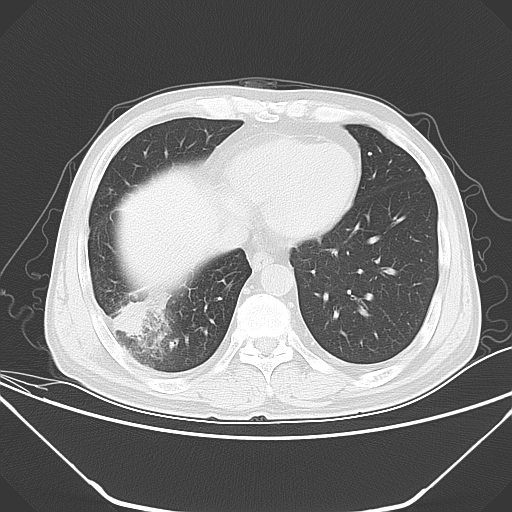
Chest CT, one axial slice. Slice 14 of 52 in the series (ordered by position). 120 kVp. Lung window (W 1500 / L -600 HU). 512 × 512 image matrix. Male patient, age 54 years. From the clinical record (not read from this slice): clinical TNM (as recorded): T2 N1 M0; histopathological grade: G3.
Annotated regions visible in this slice (bounding box drawn by a radiologist):
- lung tumour (recorded histology: adenocarcinoma): box from (x=111, y=297) to (x=150, y=338) px